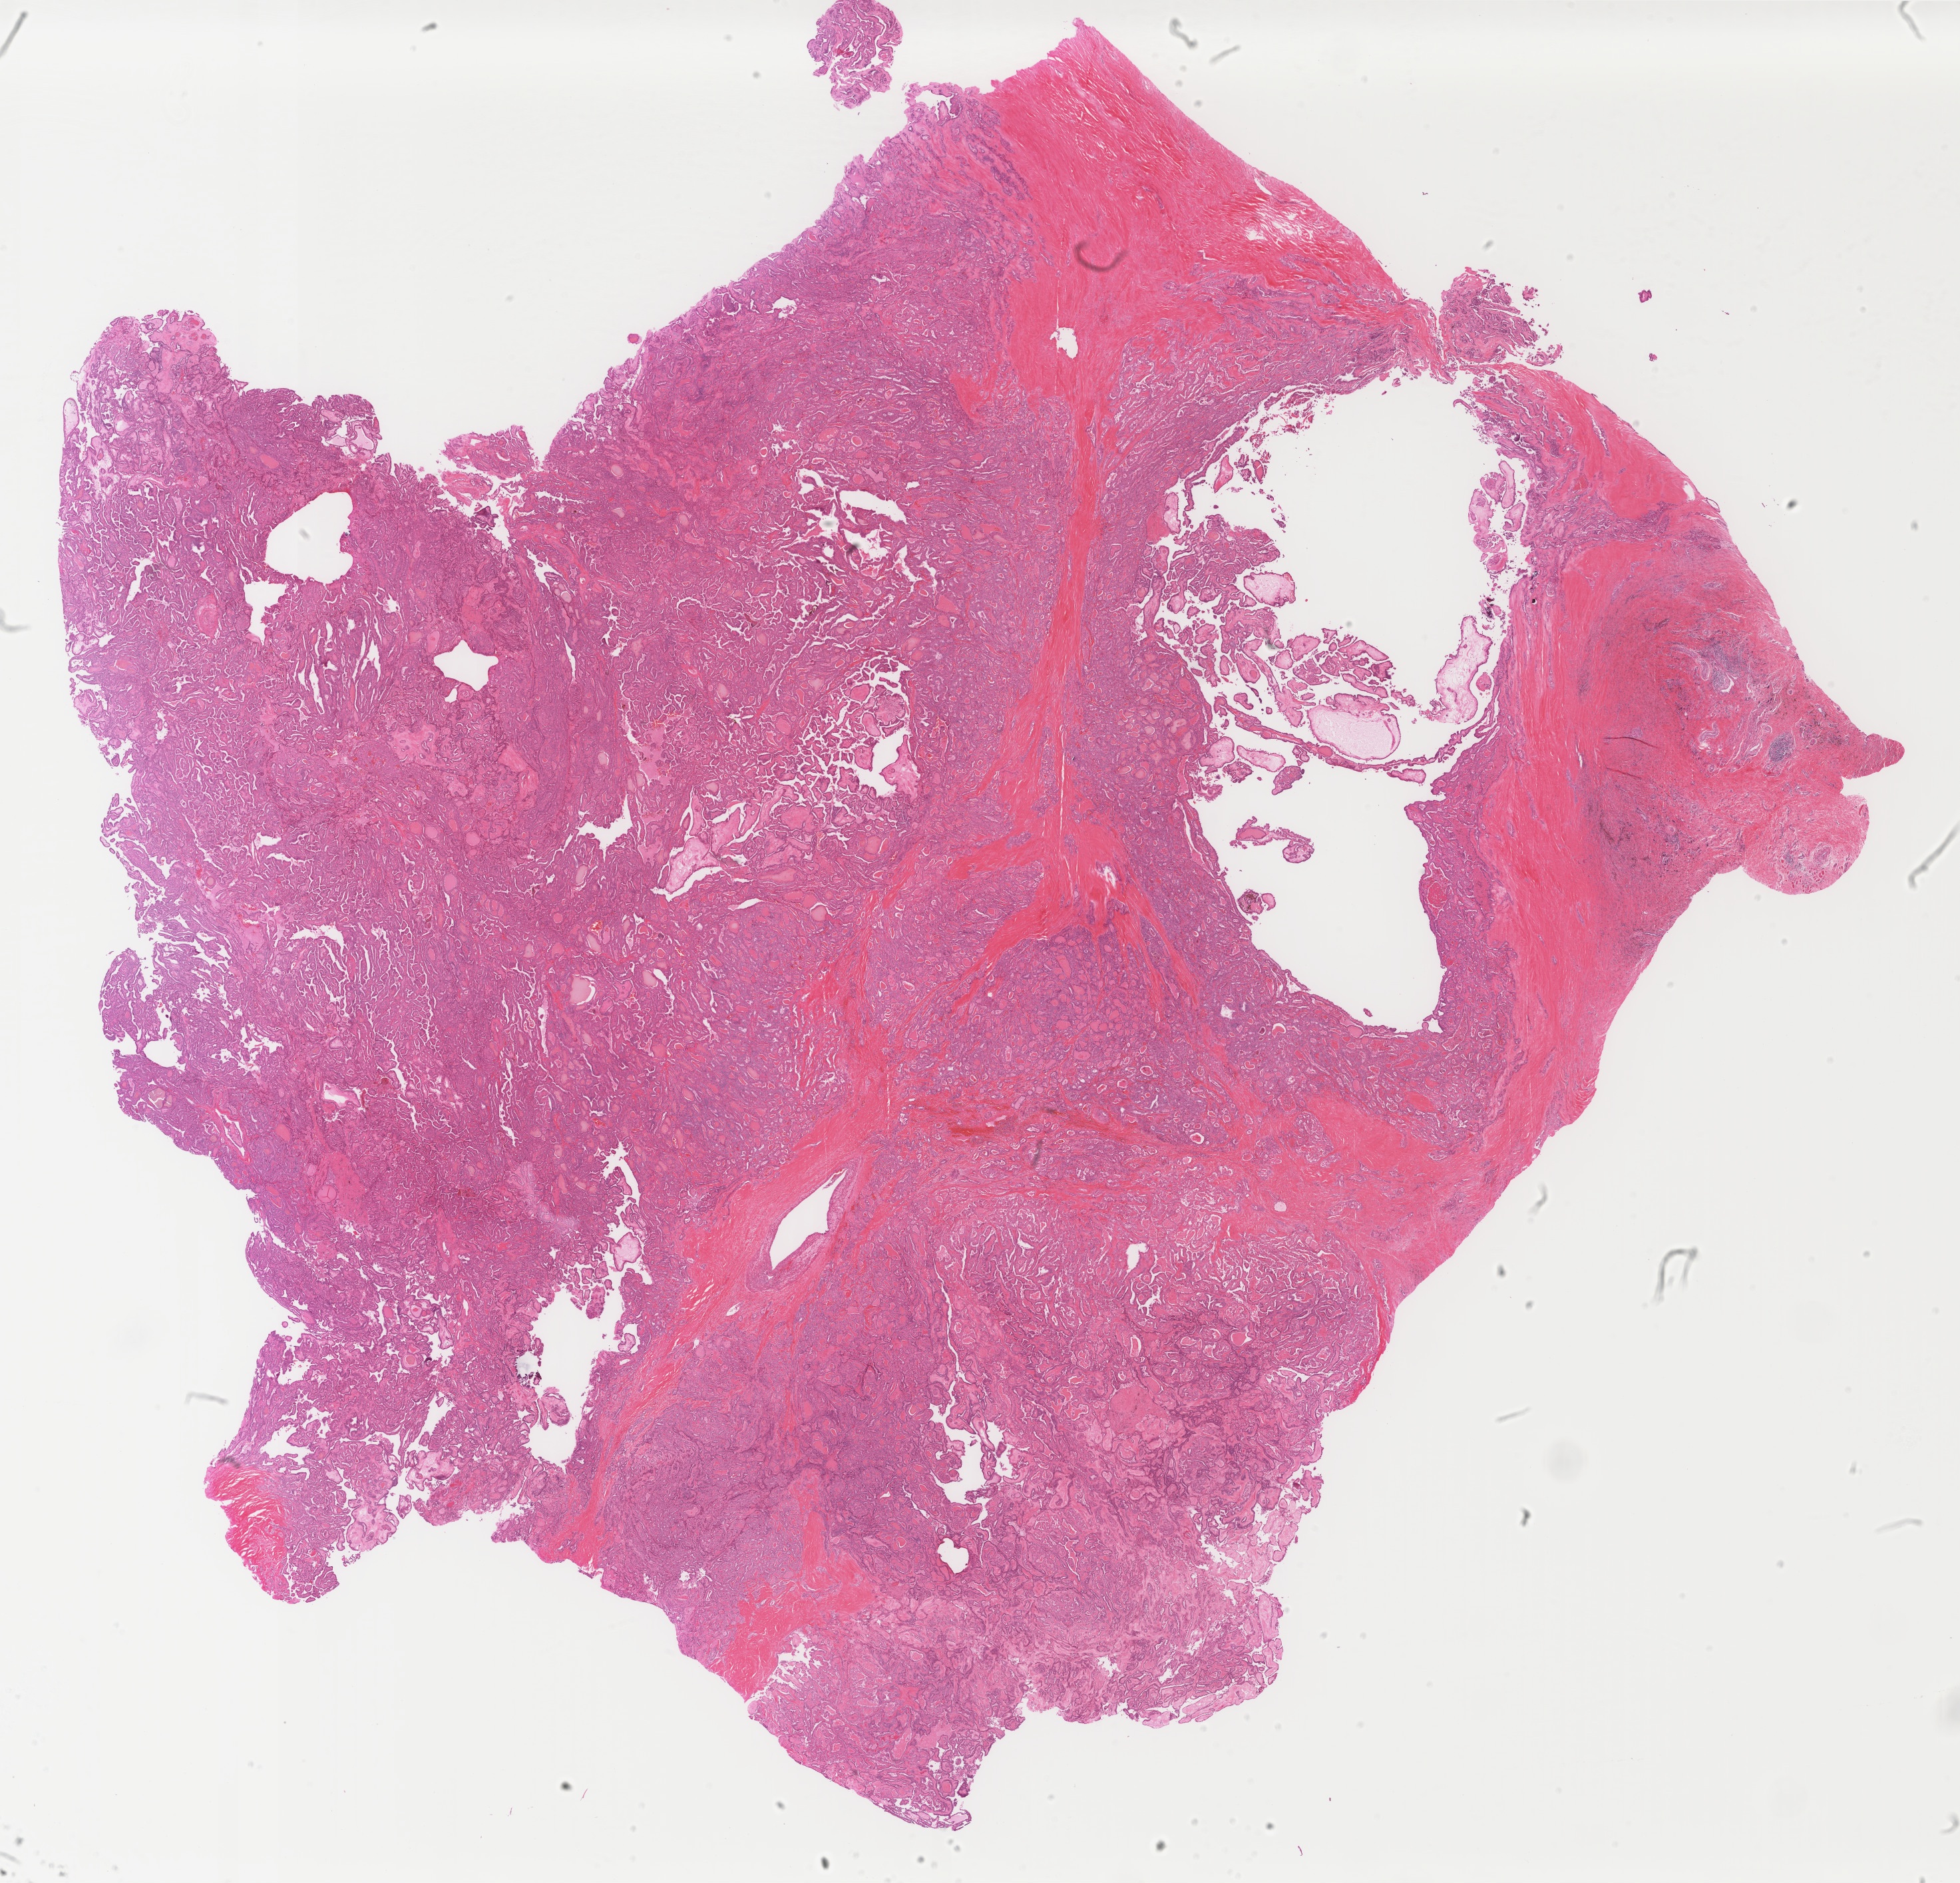
H&E whole-slide image, shown as a low-resolution overview of the whole scanned area (about 23.4 x 22.5 mm); formalin-fixed paraffin-embedded (FFPE) diagnostic section; sample: primary tumour, thyroid. Female patient; age at initial diagnosis 46 years.
AJCC pathologic stage: IVA (6th edition). Histologic diagnosis: Papillary adenocarcinoma, NOS. Lymph nodes positive (case pathology): 10 of 69 examined.